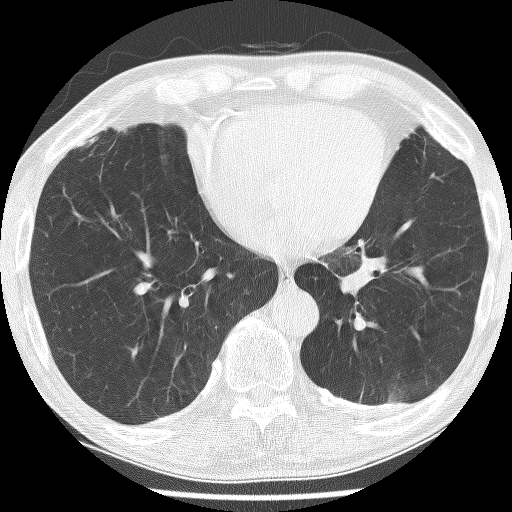
Axial slice from a low-dose chest CT screening exam; baseline annual screen; lung window (W 1500 / L -600 HU); 2.5 mm slice thickness; lung (sharp) reconstruction kernel (BONE); slice 164 of 226 in the series. Male participant, aged 74 years at enrolment. Current smoker at enrolment.
Expert reader's lesion annotation, box from (x=319, y=233) to (x=428, y=327) px. Reader record for this screening exam (exam-level; its link to the box is not recorded): non-calcified nodule or mass ≥4 mm, left lower lobe, 30 × 27 mm, spiculated (stellate) margins, soft tissue attenuation. Later outcome: lung cancer diagnosed 151 days after this screen — adenocarcinoma, NOS, left lower lobe, stage IIIA (AJCC 6th edition), 49 mm at pathology.